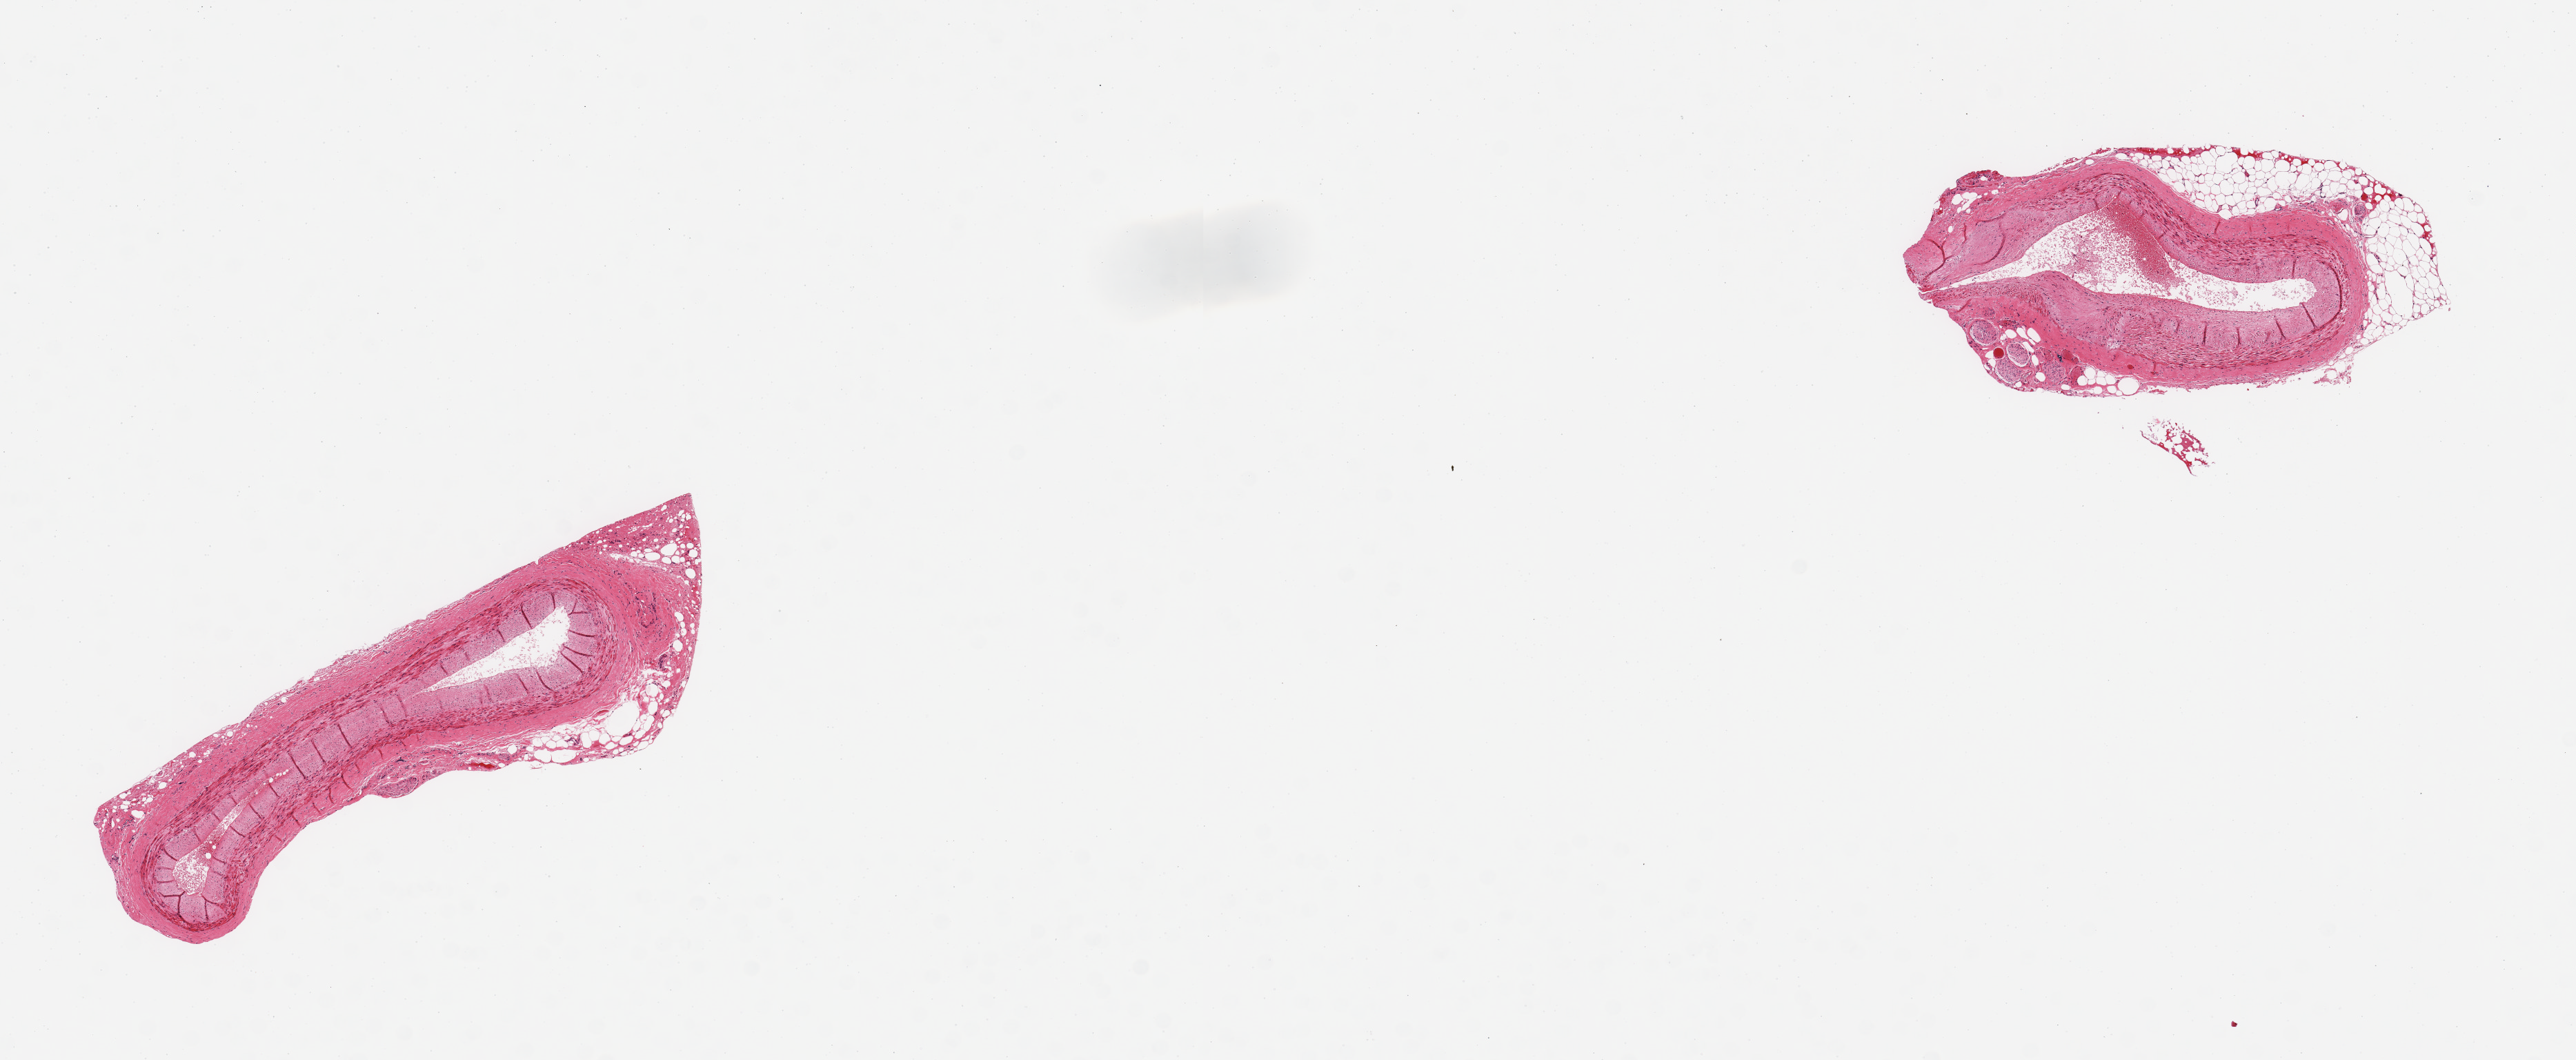
Hematoxylin and eosin (H&E) whole-slide image, brightfield, low-resolution overview of the scanned area, about 14.8 x 6.1 mm (from a 20x scan); PAXgene-fixed, paraffin-embedded tissue; target tissue: coronary artery; tissue donor sample. Female donor.
- review note (as recorded): 2 pieces; atherosclerosis, 1 piece includes residual attached fat and nerve (~40%)